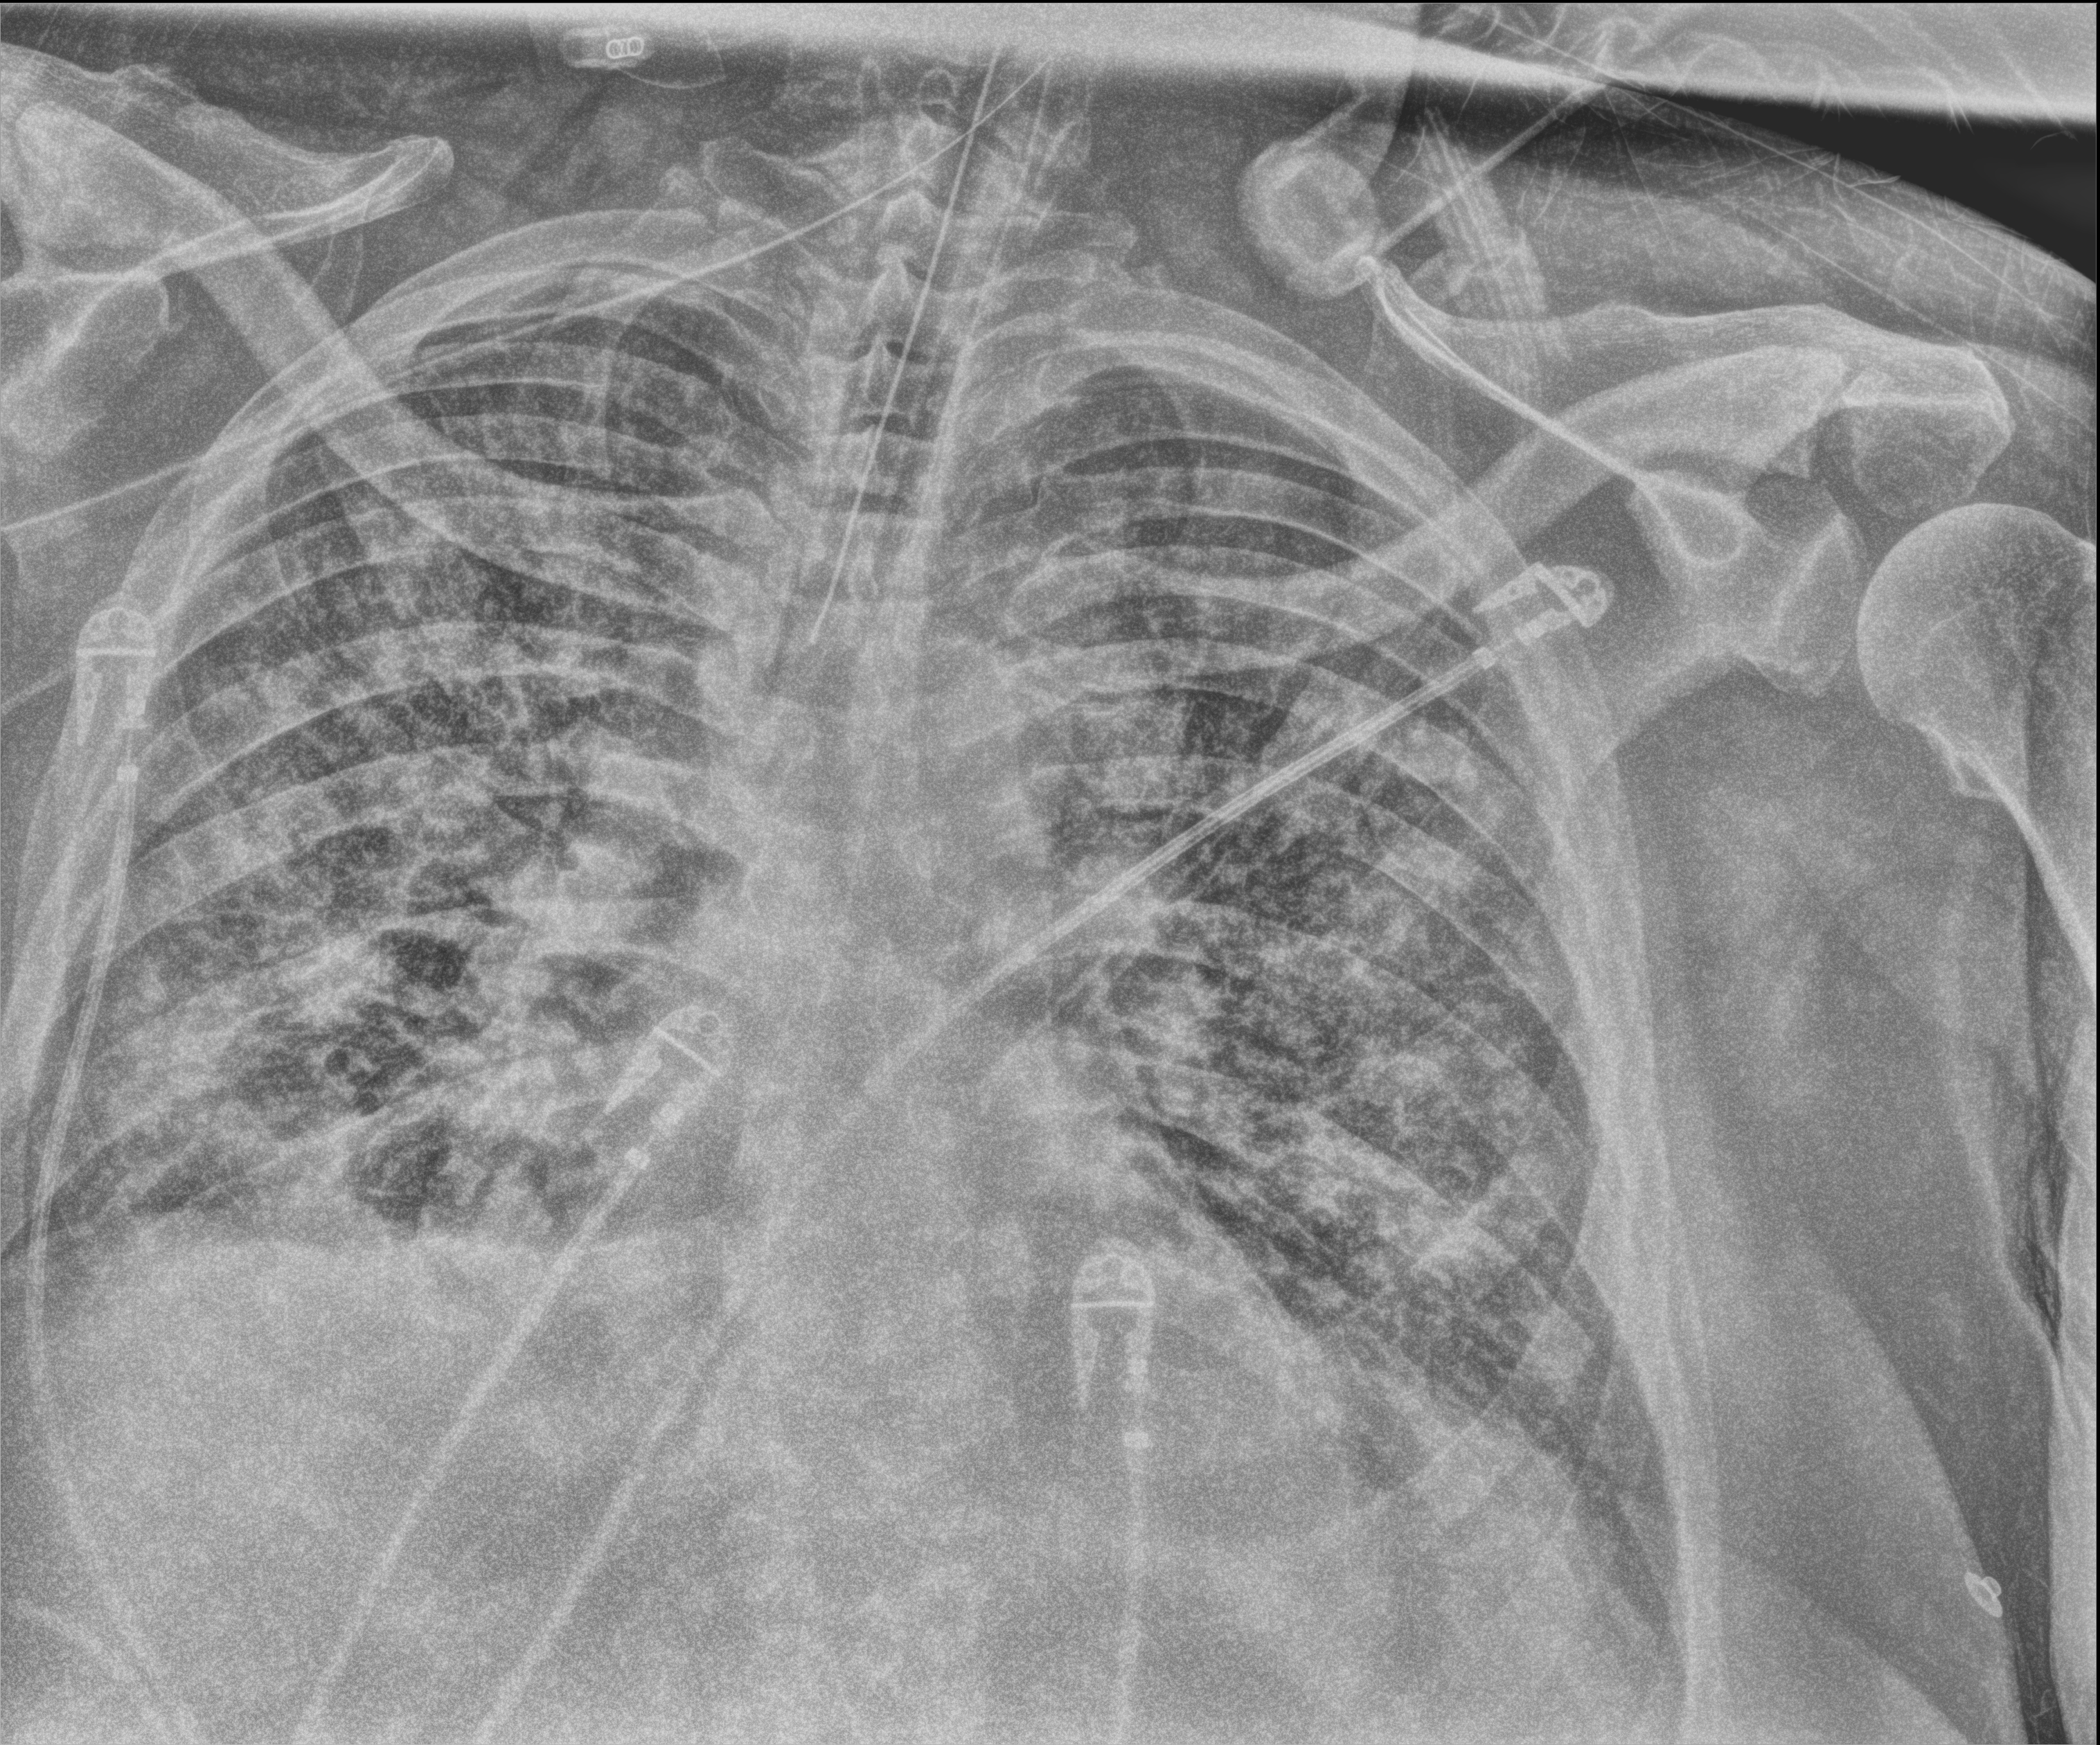
Portable chest radiograph, anteroposterior (AP) projection. Male patient hospitalised with COVID-19, age 60–74 years.
From the hospital-stay record, not from the radiograph (when in the stay this image was taken is not recorded):
- smoking status (admission record): never